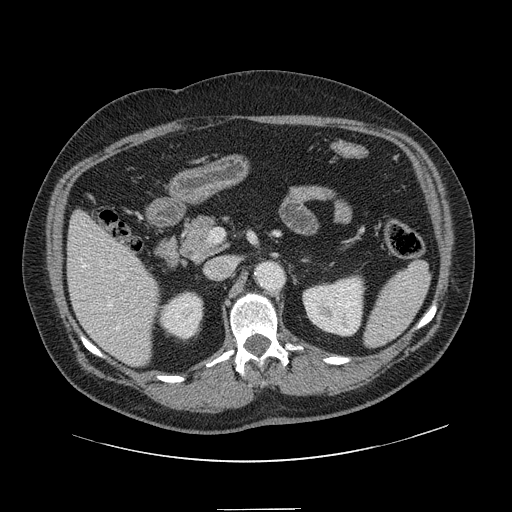
Contrast-enhanced abdominal CT, one axial slice; 120 kVp; intravenous contrast given; soft-tissue window (W 400 / L 40 HU); 2.5 mm slice thickness; 512 × 512 image matrix. Male patient, age 61 years. From the clinical record (not read from this slice): diagnosis: colorectal cancer liver metastases, imaged before liver resection; multiple liver metastases: yes; largest metastasis: 2.6 cm.
Outlined on this slice (manually delineated by an expert):
- hepatic veins: bounding box <83,260,119,330> (left, top, right, bottom; pixels)
- liver: <69,212,160,366>
- planned liver remnant (the part of the liver to remain after resection): <69,212,160,364>